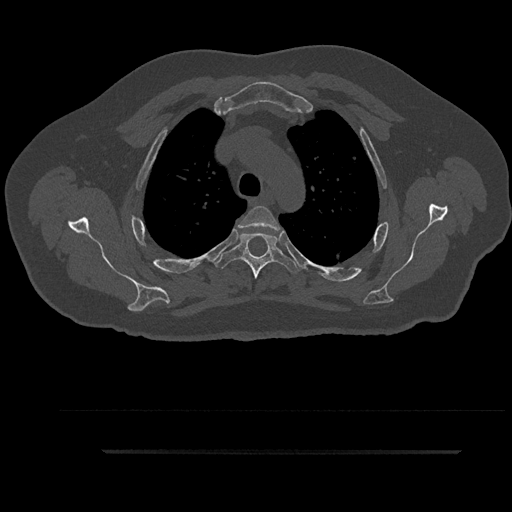
CT including the spine, one axial slice. Position 686 of 797 along the scan axis. Reconstruction kernel Br40s/3. Bone window (W 1800 / L 400 HU). 0.5 mm slice thickness. 512 × 512 image matrix, field of view 432 × 432 mm. Male patient, age 63 years. From the clinical record (not read from this slice): primary cancer: renal.
Annotated regions visible in this slice (semi-automatic segmentation, software-assisted and operator-edited):
- T3 vertebra: bounding box [x1, y1, x2, y2] px = [238, 206, 280, 234]
- T4 vertebra: [214, 233, 300, 279]